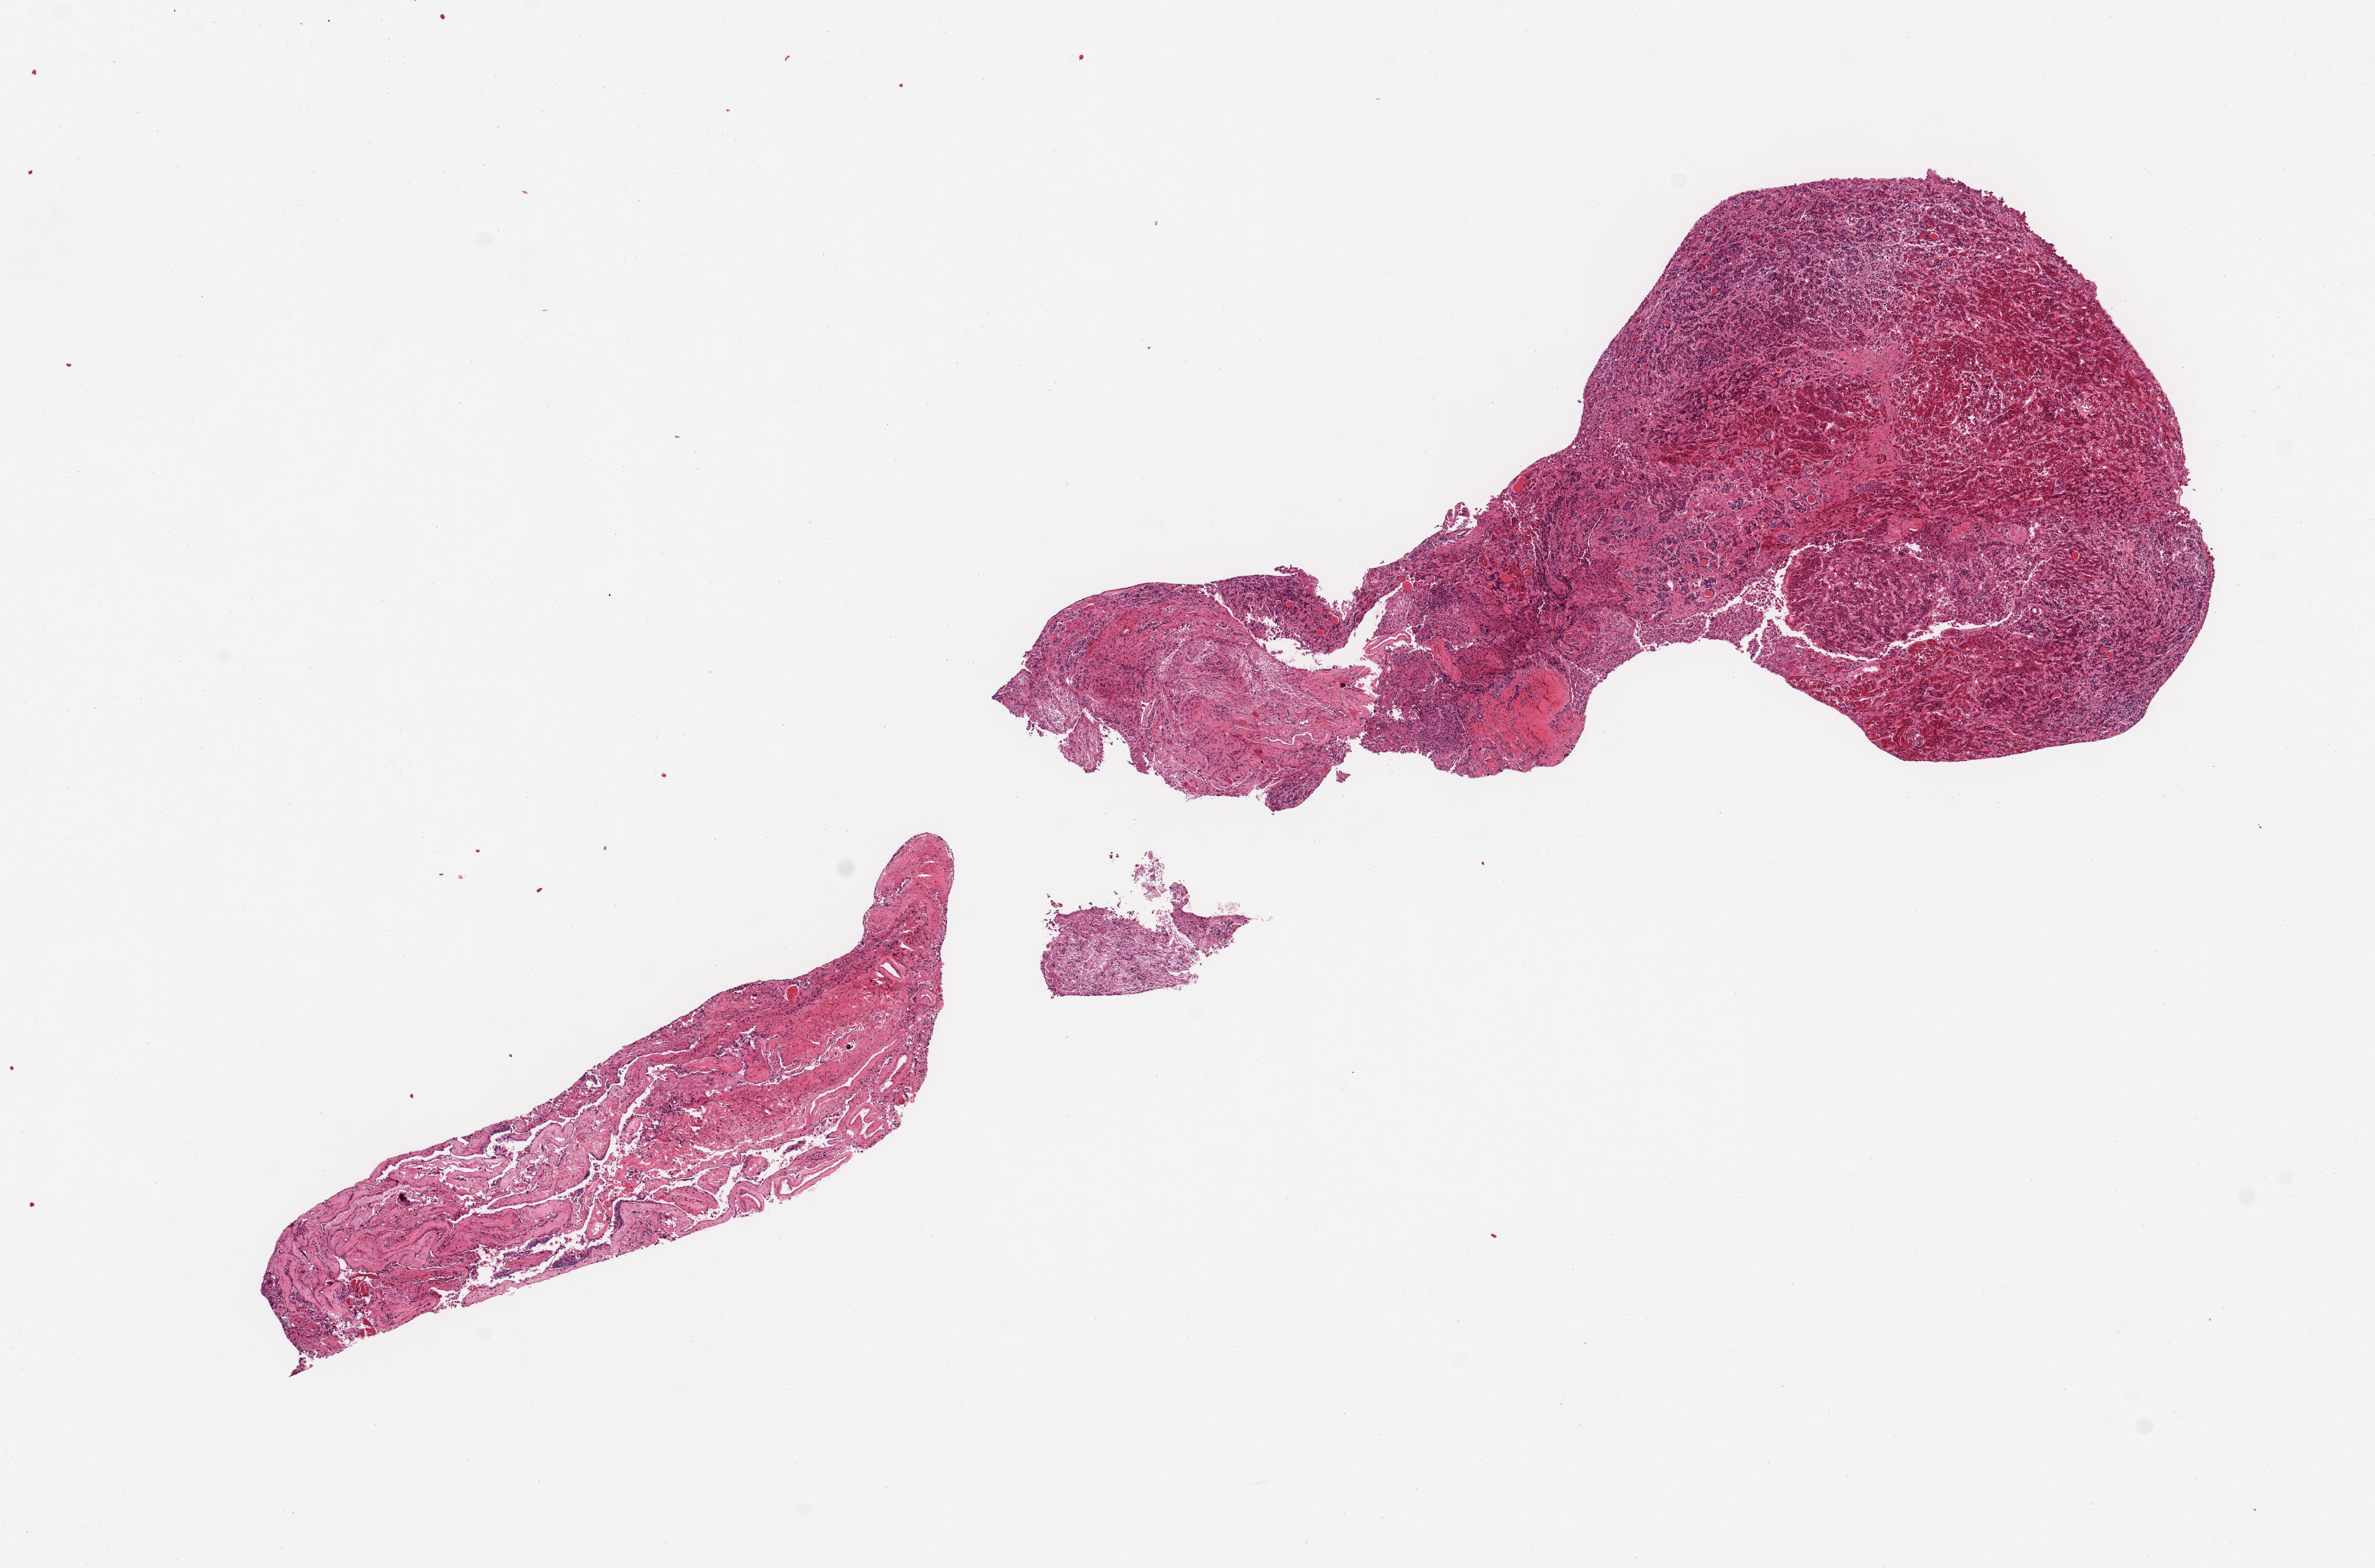
Haematoxylin and eosin whole-slide image, whole scanned area (about 14.8 x 9.8 mm) shown as a low-resolution overview, PAXgene-fixed, paraffin-embedded tissue, section of pituitary (target tissue), donor tissue sample. Donor sex: male.
Review note (as recorded): 1 fragmented piece labeled; anterior is largest.